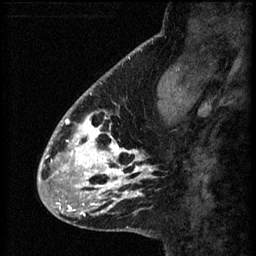
Breast MRI (dynamic contrast-enhanced), one sagittal slice; position 18 of 60 along the scan axis; 3 images stored at this slice position (order not interpretable as contrast timing); 1.5 T; TE 4.2 ms, TR 8.2 ms; 2.2 mm slice thickness; 256 × 256 image matrix. Patient: female, 41 years.
Annotated regions visible in this slice (semi-automatically segmented with operator editing):
- analysis volume of interest (the breast-tissue region the enhancement analysis was run in; not a lesion): box from (x=56, y=104) to (x=155, y=207) px
- tumour enhancement mask (voxels above the 70 % enhancement threshold inside the analysis volume of interest): (x=56, y=108)–(x=154, y=207)